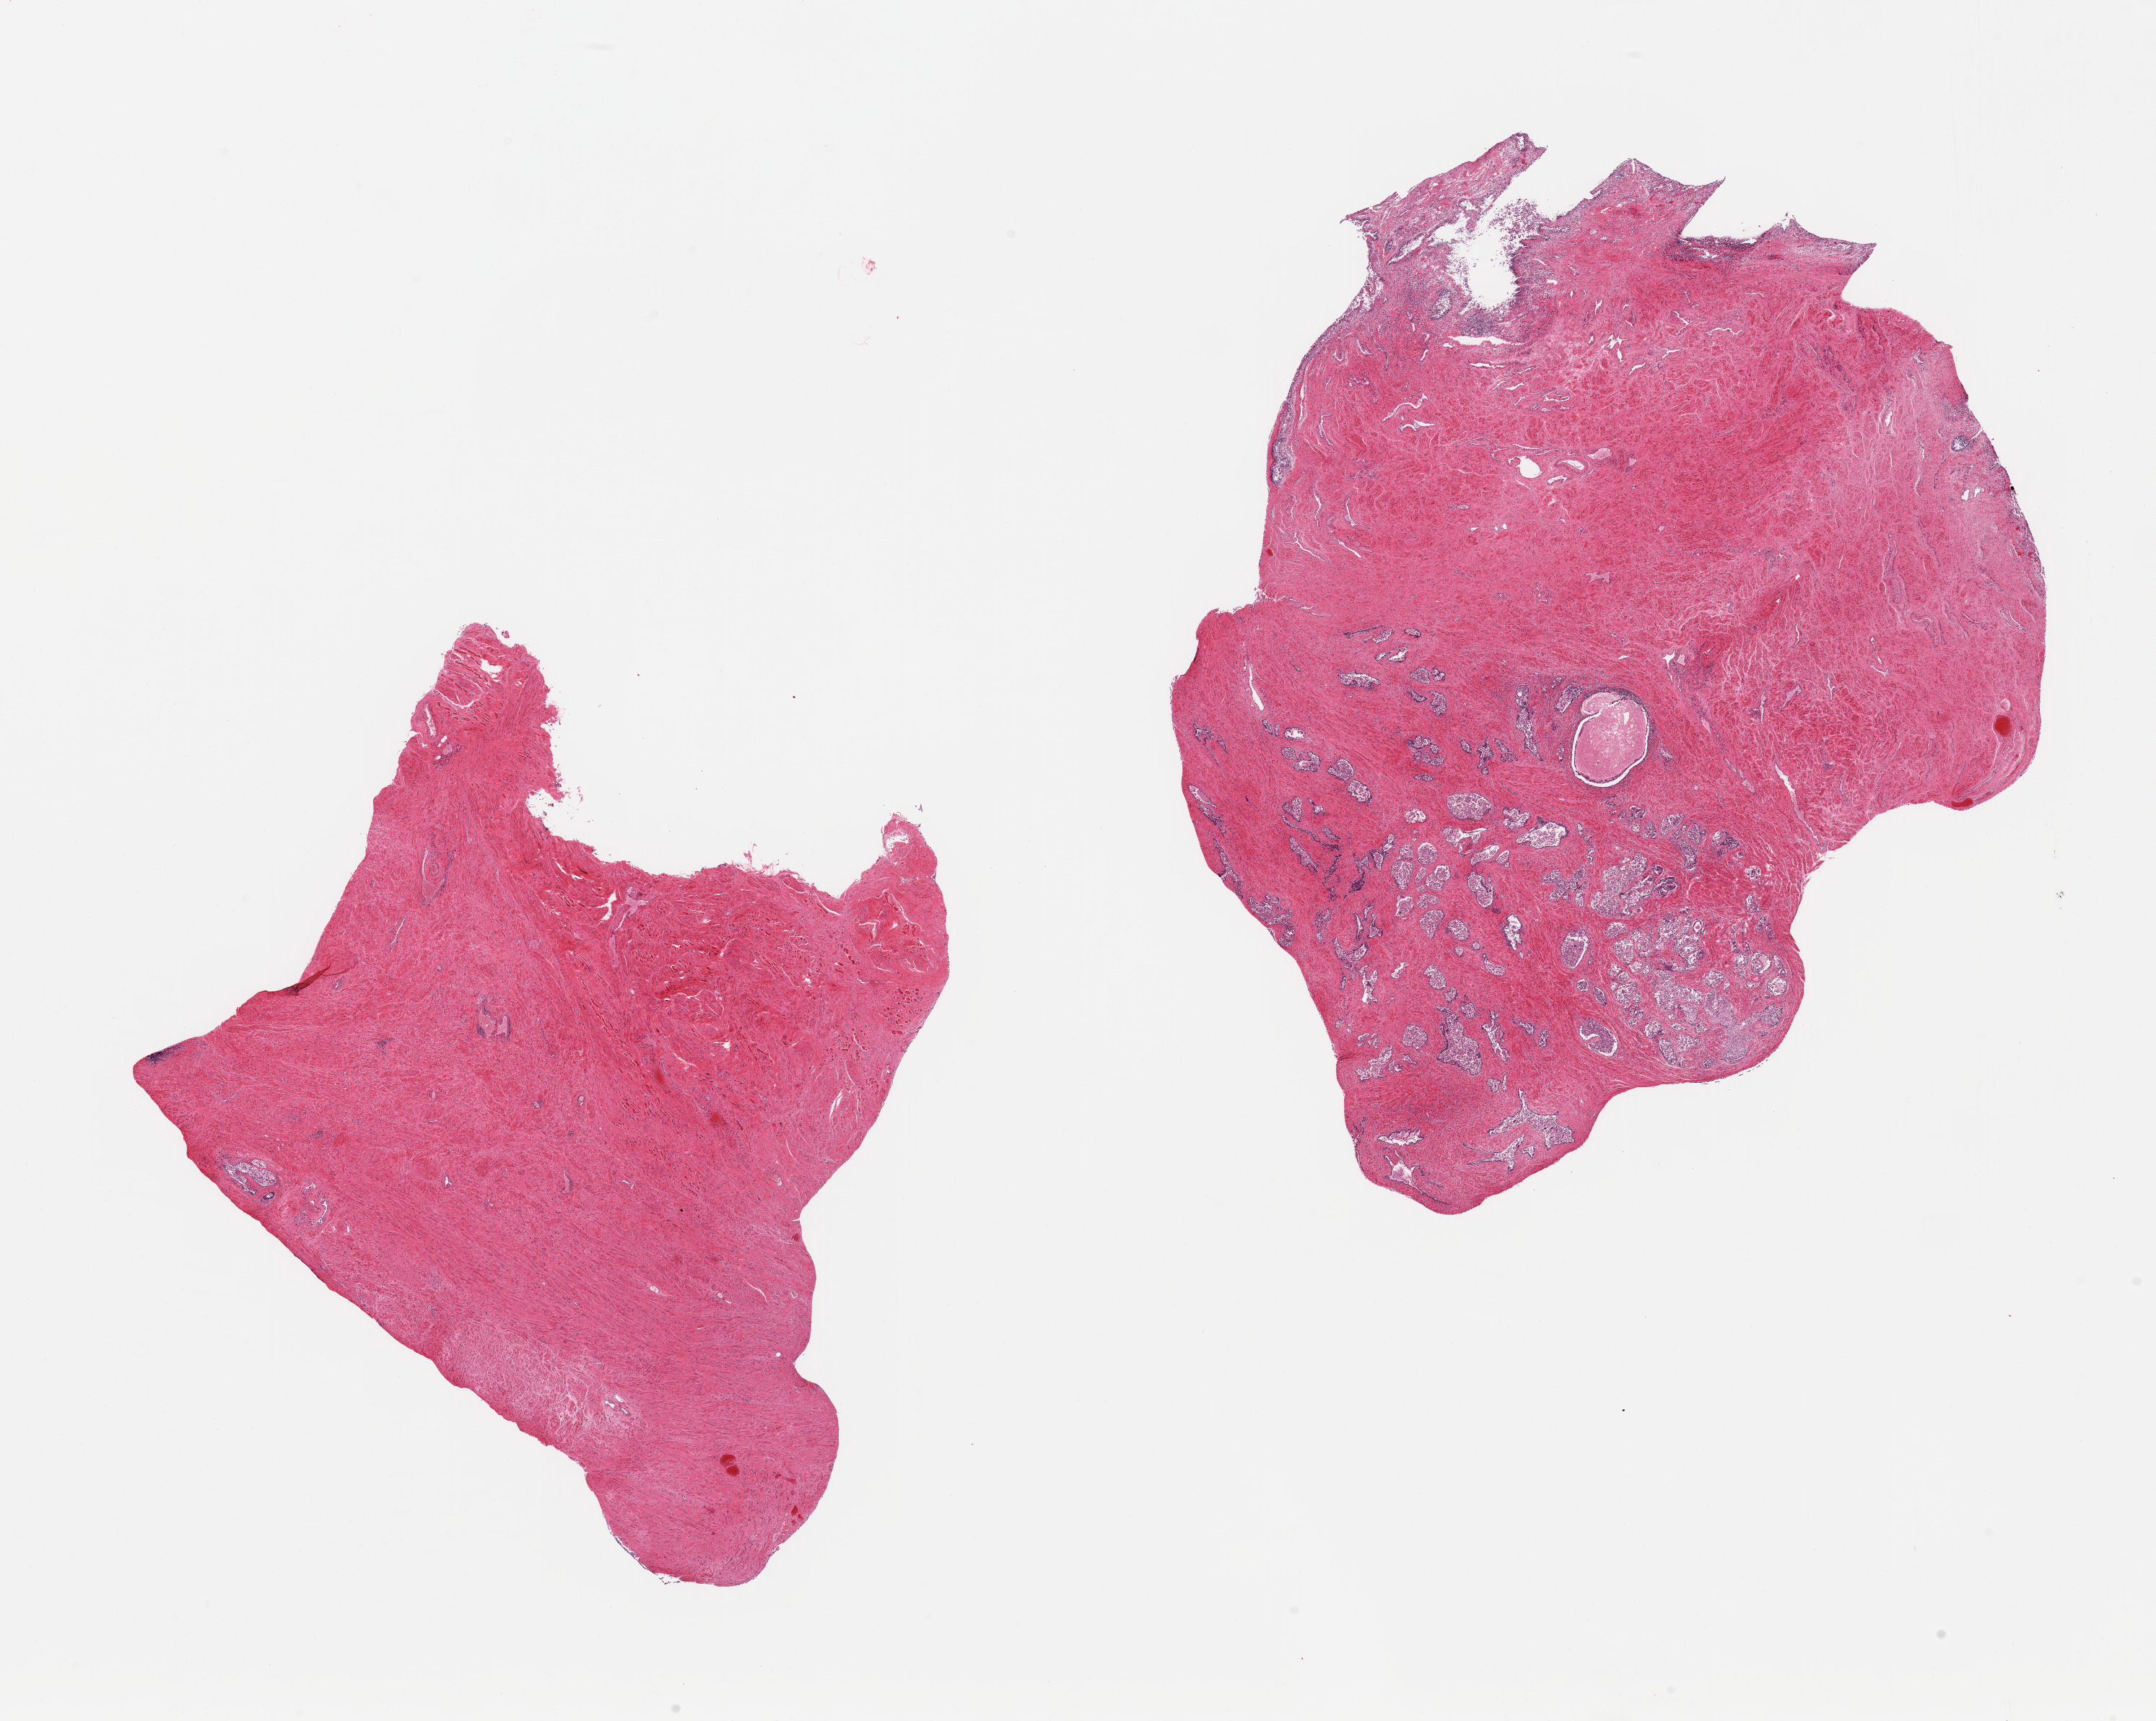
Whole-slide image, hematoxylin and eosin (H&E) stain — shown as a low-resolution overview of the whole scanned area (about 23.6 x 18.9 mm); PAXgene-fixed, paraffin-embedded tissue; section of prostate (target tissue); tissue donor sample. Male donor.
Review note (as recorded): 2 pieces; glands severely autolyzed, muscular stroma intact; 1 piece is virtually all stroma, other is half glandular.